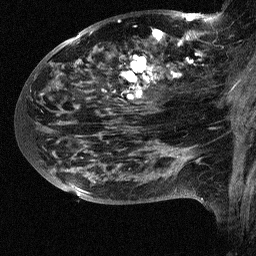
Breast MRI (dynamic contrast-enhanced), one sagittal slice. Slice 35 of 64 in the series (ordered by position). Dynamic contrast-enhanced study with each time point stored as its own series, time point 2 of 3 at this slice position (early post-contrast, ordered by acquisition time). 1.5 T. TE 4.5 ms, TR 11 ms. 2.5 mm slice thickness. 256 × 256 image matrix. Female patient, age 38 years. From the clinical record (not read from this slice): setting: breast cancer imaged before/during neoadjuvant chemotherapy; receptor status: HR-positive, HER2-negative.
Outlined on this slice (semi-automatic segmentation, software-assisted and operator-edited):
- analysis volume of interest (the breast-tissue region the enhancement analysis was run in; not a lesion): bounding box [x1, y1, x2, y2] px = [88, 18, 252, 126]
- tumour enhancement mask (voxels above the 90 % enhancement threshold inside the analysis volume of interest): [119, 18, 199, 97]